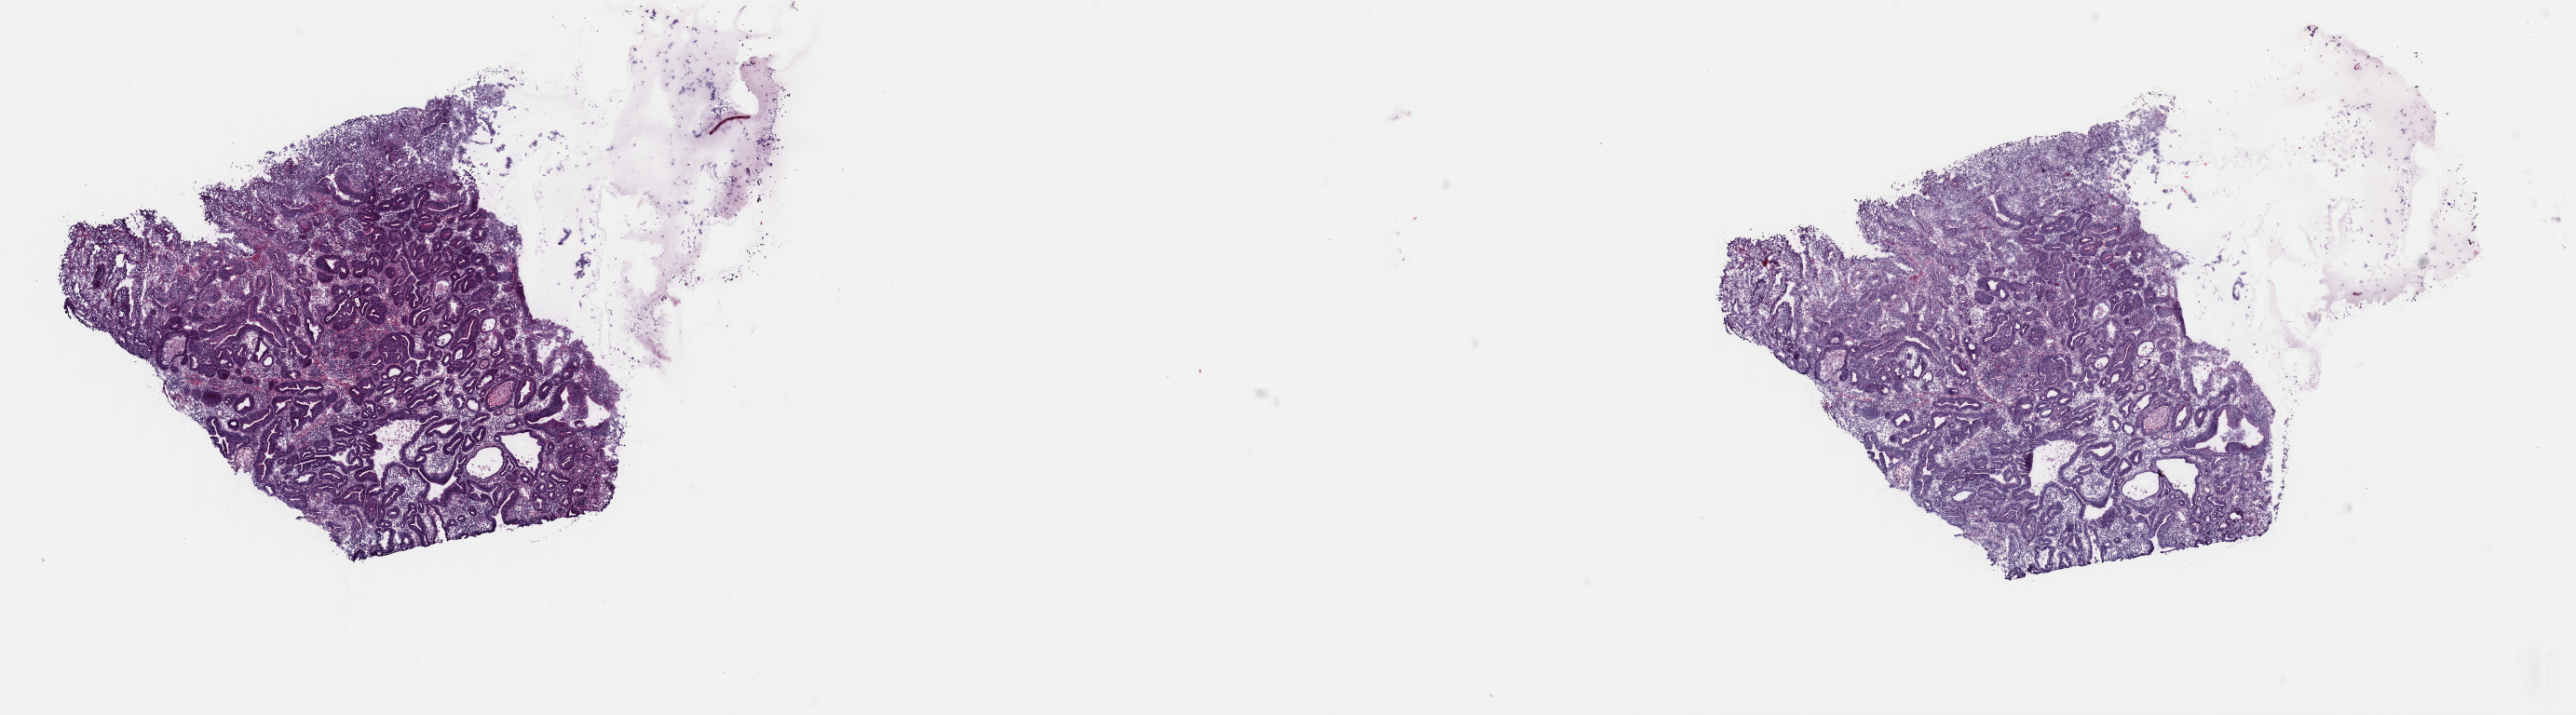
Hematoxylin and eosin (H&E) stained whole-slide image, shown as a low-resolution overview of the whole scanned area (about 21.9 x 6.1 mm, slide scanned at 40x). Frozen section. Sample: primary tumour, esophagus. Male, age 74 years at initial diagnosis. Histologic grade: GX (grade cannot be assessed). Slide review estimates, as recorded: tumour cells 70%, tumour nuclei 85%, normal cells 0%, stromal cells 25%, necrosis 5%. Infiltration values recorded for this section: lymphocyte infiltration 5%, monocyte infiltration 0%, neutrophil infiltration 0%.
Pathologic diagnosis: Adenocarcinoma, NOS (lower third of esophagus). TNM: T1 N0 M0. Lymph nodes positive (case pathology): 0 of 10 examined. AJCC pathologic stage: I (7th edition).